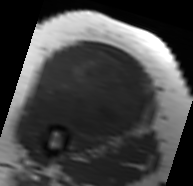
MRI of an extremity soft-tissue mass, one axial slice. MR volume resampled by the dataset authors to the PET/CT grid (not the native acquisition matrix). 193 × 186 image matrix, field of view 188 × 182 mm. Female patient. Case-level facts recorded for this patient, not image findings: histological type: malignant solitary fibrous tumor; grade: intermediate; site of the primary tumour: right thigh.
Annotated regions visible in this slice (expert contour drawn on MRI and transferred to this co-registered scan by the dataset authors):
- gross tumour volume including surrounding oedema: bounding box <24,44,153,141> (left, top, right, bottom; pixels)
- gross tumour volume (mass): <29,44,148,139>